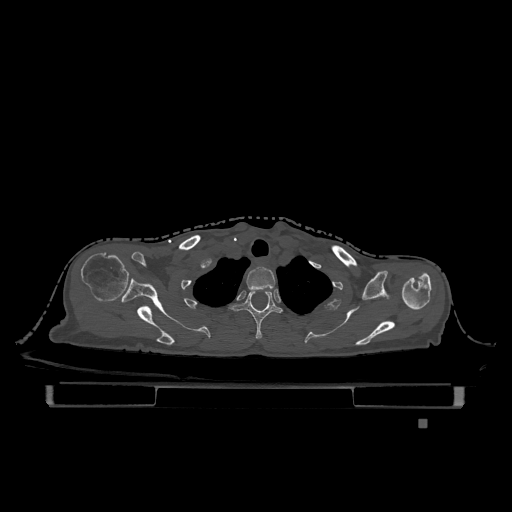
CT including the spine, one axial slice; position 970 of 1317 along the scan axis; bone window (W 1800 / L 400 HU); 0.5 mm slice thickness; 512 × 512 image matrix, field of view 500 × 500 mm. Patient: female, 74 years. Case-level facts recorded for this patient, not image findings: primary cancer: lung; vertebrae with lytic lesions (as recorded): T1, T4, T5, T6, L4, L5.
Outlined on this slice (semi-automatic segmentation, software-assisted and operator-edited):
- T1 vertebra: bounding box <246,266,276,291> (left, top, right, bottom; pixels)
- T2 vertebra: <229,290,282,339>